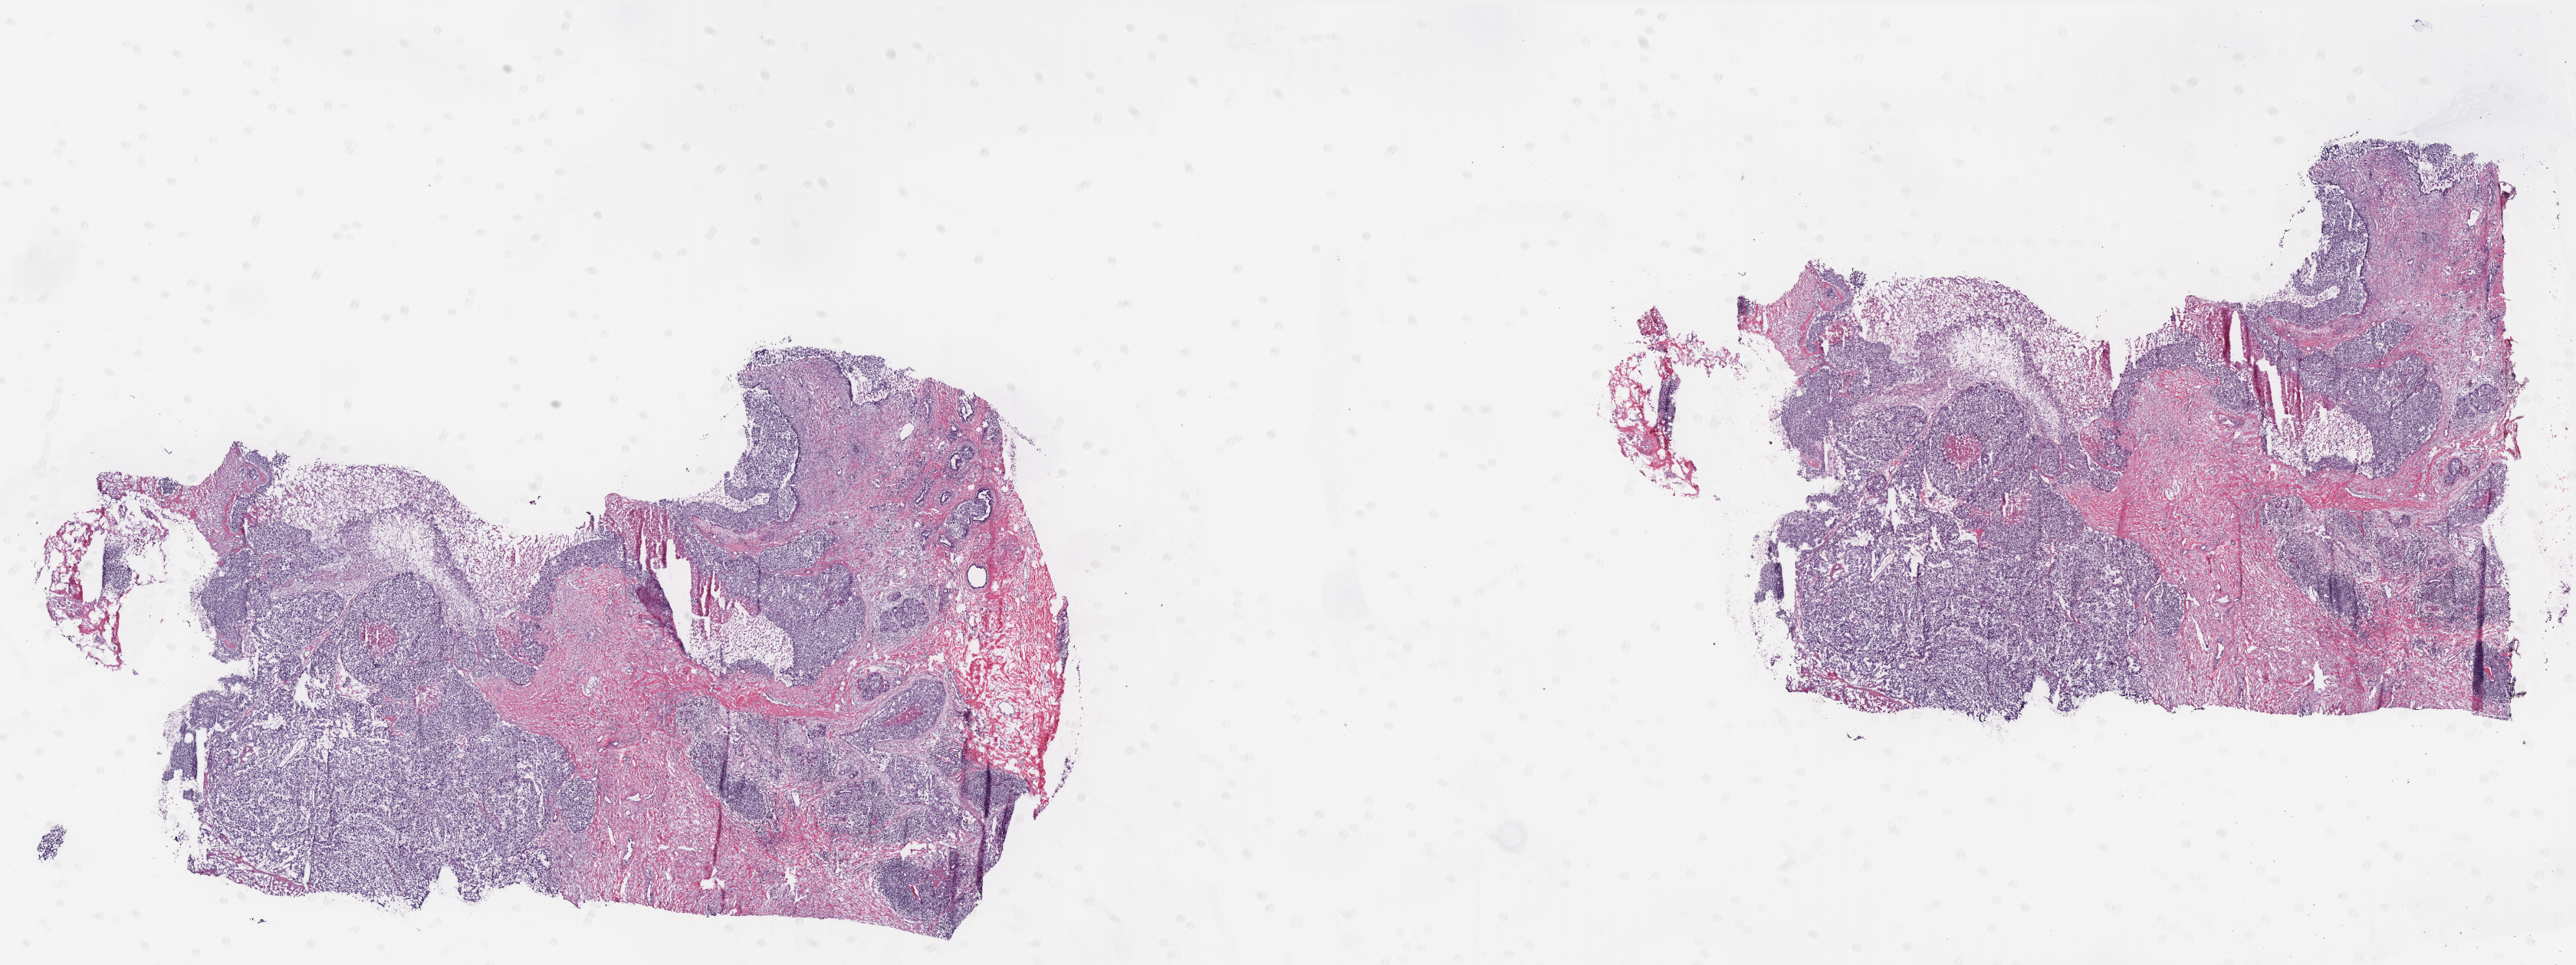
Whole-slide histology image, Hematoxylin and eosin (H&E) stained, whole scanned area (about 26.9 x 10.1 mm) shown as a low-resolution overview, frozen section, primary tumour sample from the breast. Female patient; age at initial diagnosis 45 years. Pathologist review of this section (percent, as recorded): tumour cells 50%, tumour nuclei 65%.
Pathologic diagnosis: Infiltrating duct carcinoma, NOS.